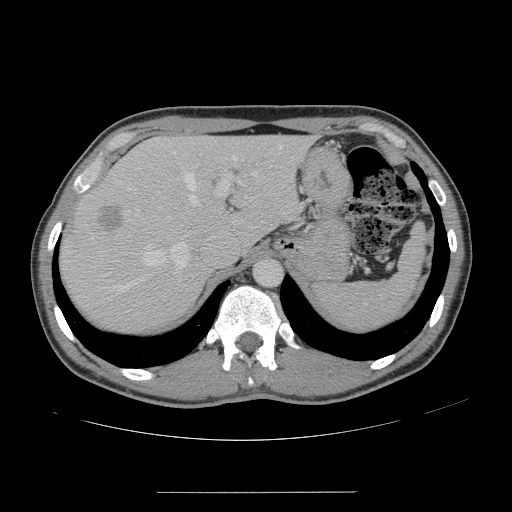
Contrast-enhanced abdominal CT, one axial slice; slice 113 of 178 in the series (ordered by position); 120 kVp; soft-tissue window (W 400 / L 40 HU); 512 × 512 image matrix, field of view 401 × 401 mm. Male patient, age 53 years. From the clinical record (not read from this slice): diagnosis: colorectal cancer liver metastases, imaged before liver resection; multiple liver metastases: yes; largest metastasis: 2.4 cm; disease in both lobes: no.
Annotated regions visible in this slice (outlined manually by an expert reader):
- hepatic veins: bounding box (x1, y1, x2, y2) in pixels: (115, 145, 282, 291)
- liver: (62, 136, 309, 332)
- planned liver remnant (the part of the liver to remain after resection): (147, 136, 310, 247)
- portal vein (with intrahepatic branches): (138, 170, 242, 211)
- liver metastasis: (98, 206, 124, 232)